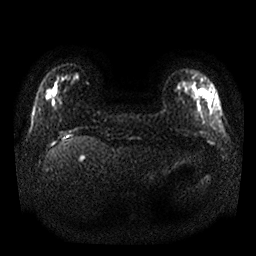
Breast MRI, one axial slice. Position 3 of 25 along the scan axis. Diffusion-weighted series; image 2 of 4 stored at this slice position (different b-values; order by instance number). 1.5 T. 4 mm slice thickness. 256 × 256 image matrix, field of view 340 × 340 mm. Female patient.
Annotated regions visible in this slice (expert manual segmentation):
- tumour on diffusion-weighted imaging: bounding box [x1, y1, x2, y2] px = [197, 89, 214, 114]